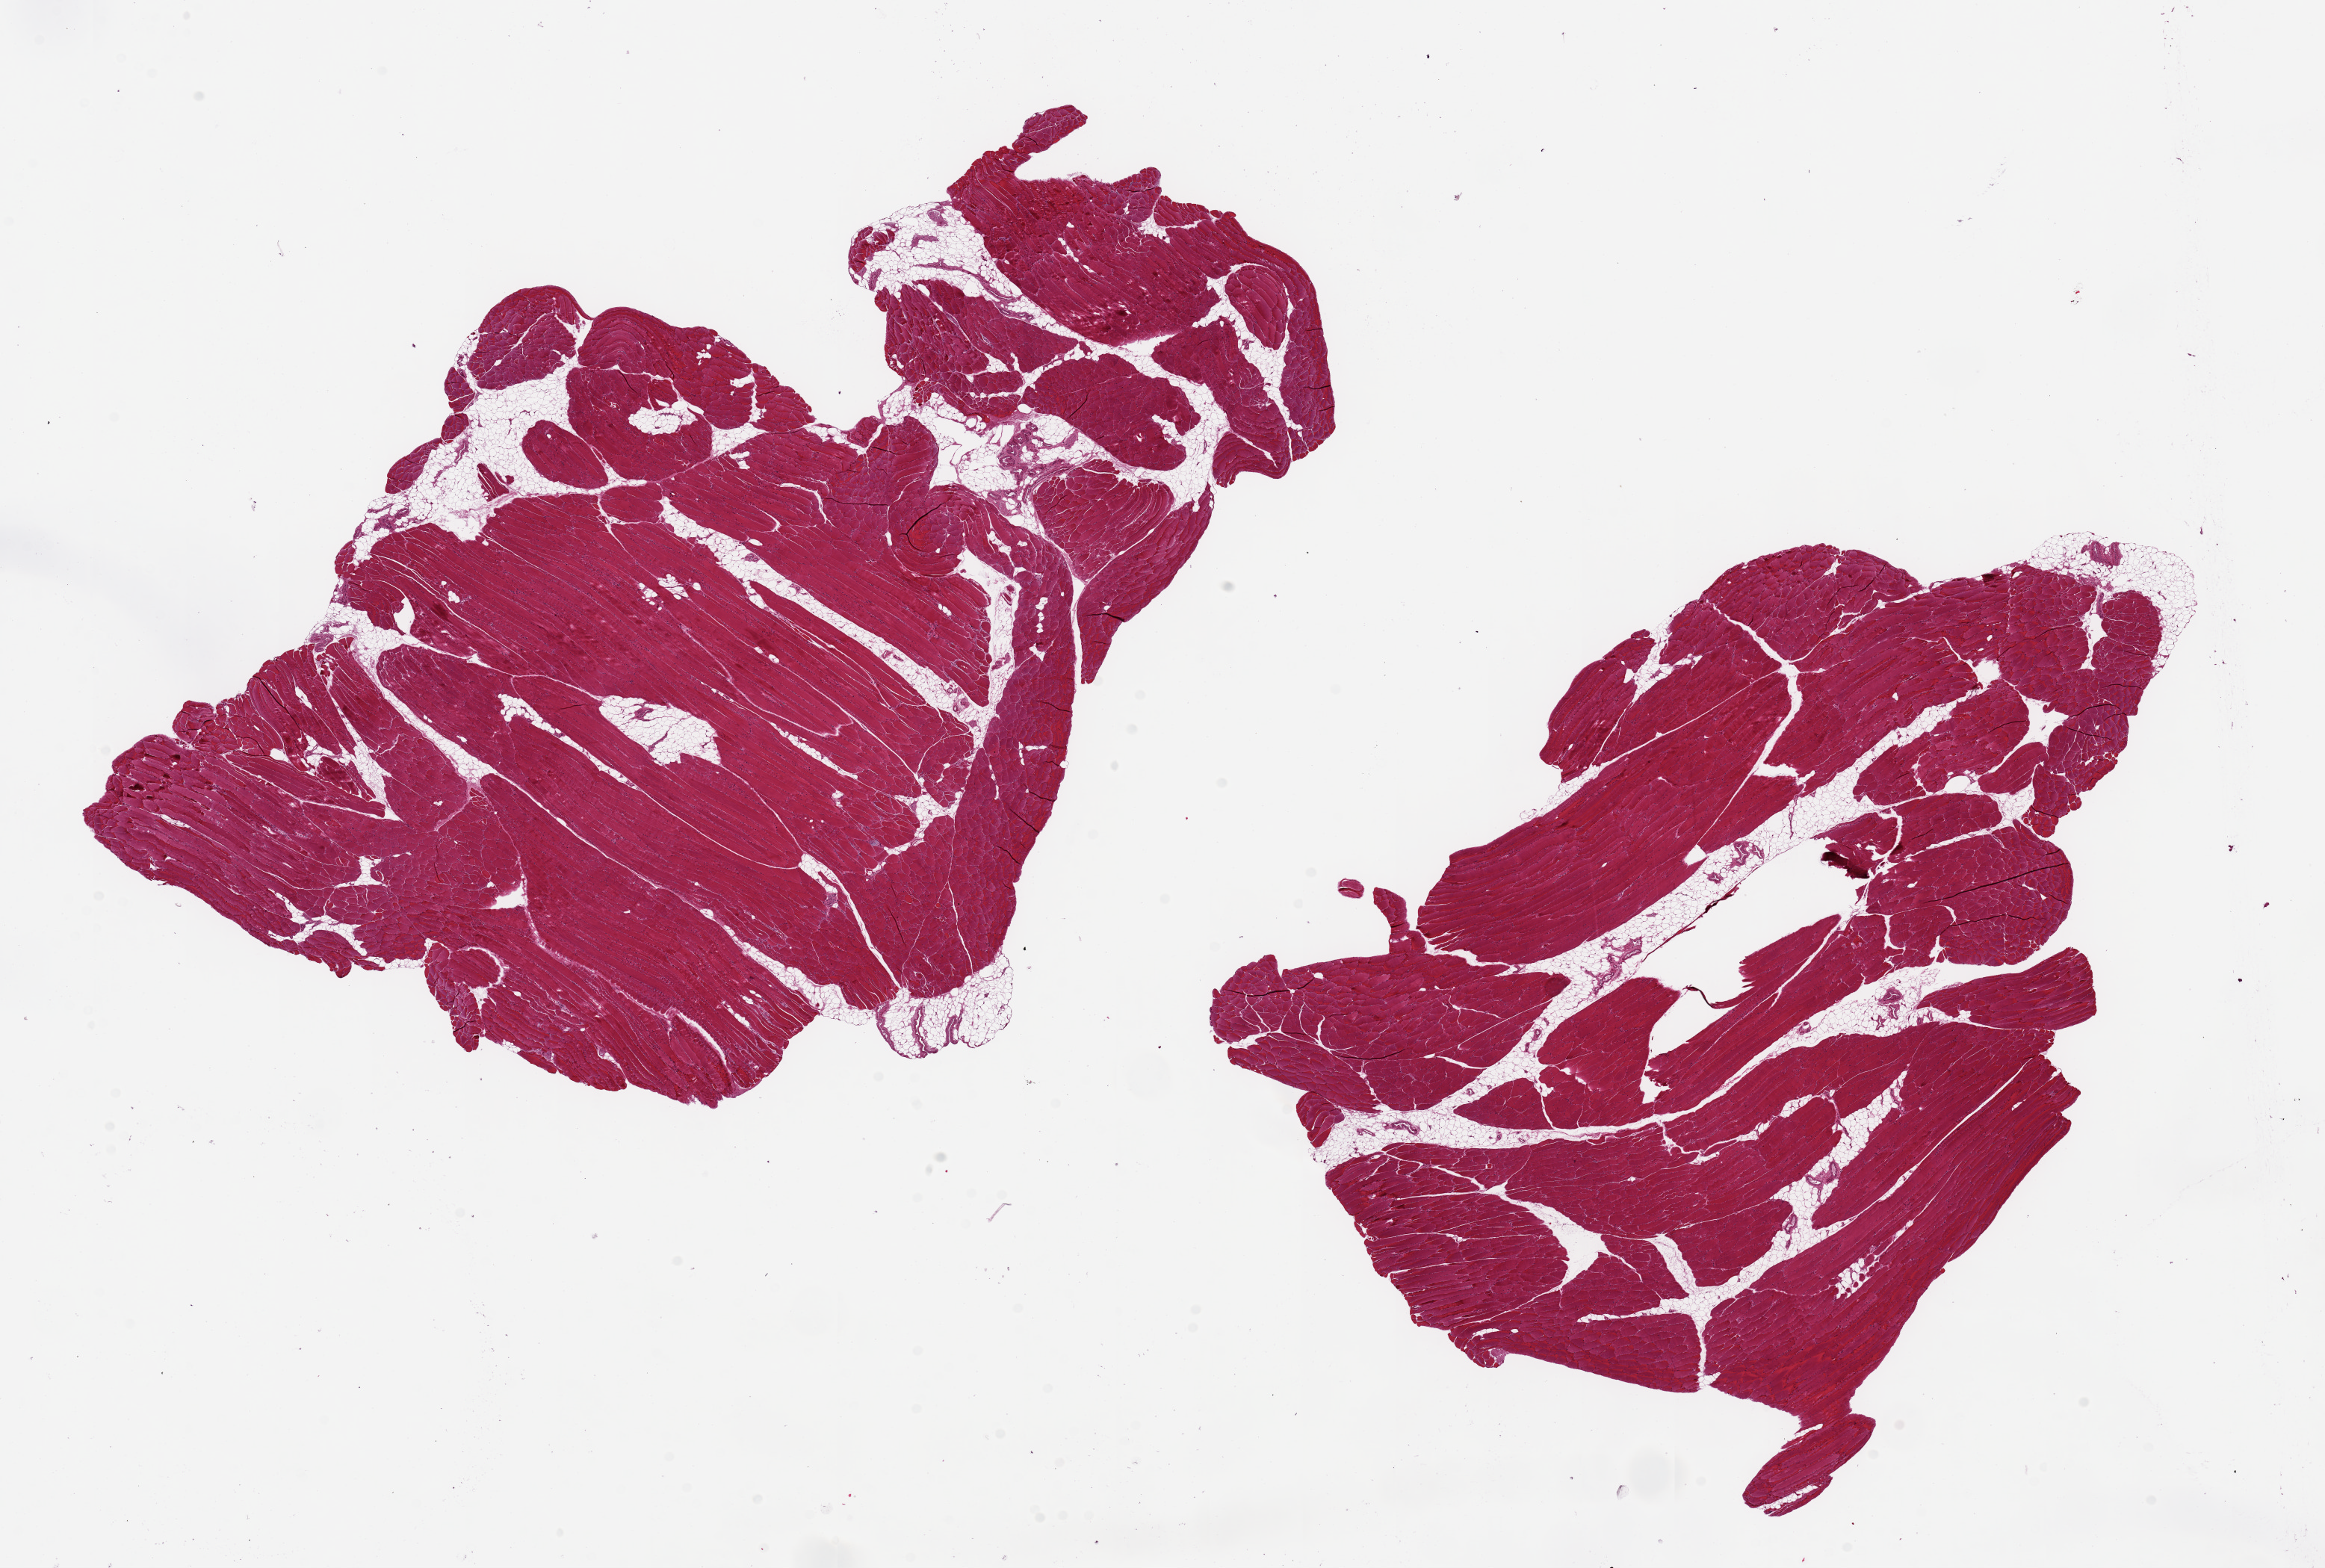
H&E whole-slide image, brightfield, shown as a low-resolution overview of the whole scanned area (about 24.6 x 16.6 mm). PAXgene-fixed paraffin-embedded (PFPE) section. Target tissue: skeletal muscle. Tissue donor sample. Donor sex: female.
Review note (as recorded): 2 pieces, 13x9 & 11x8mm; ~10% interstitial fat.